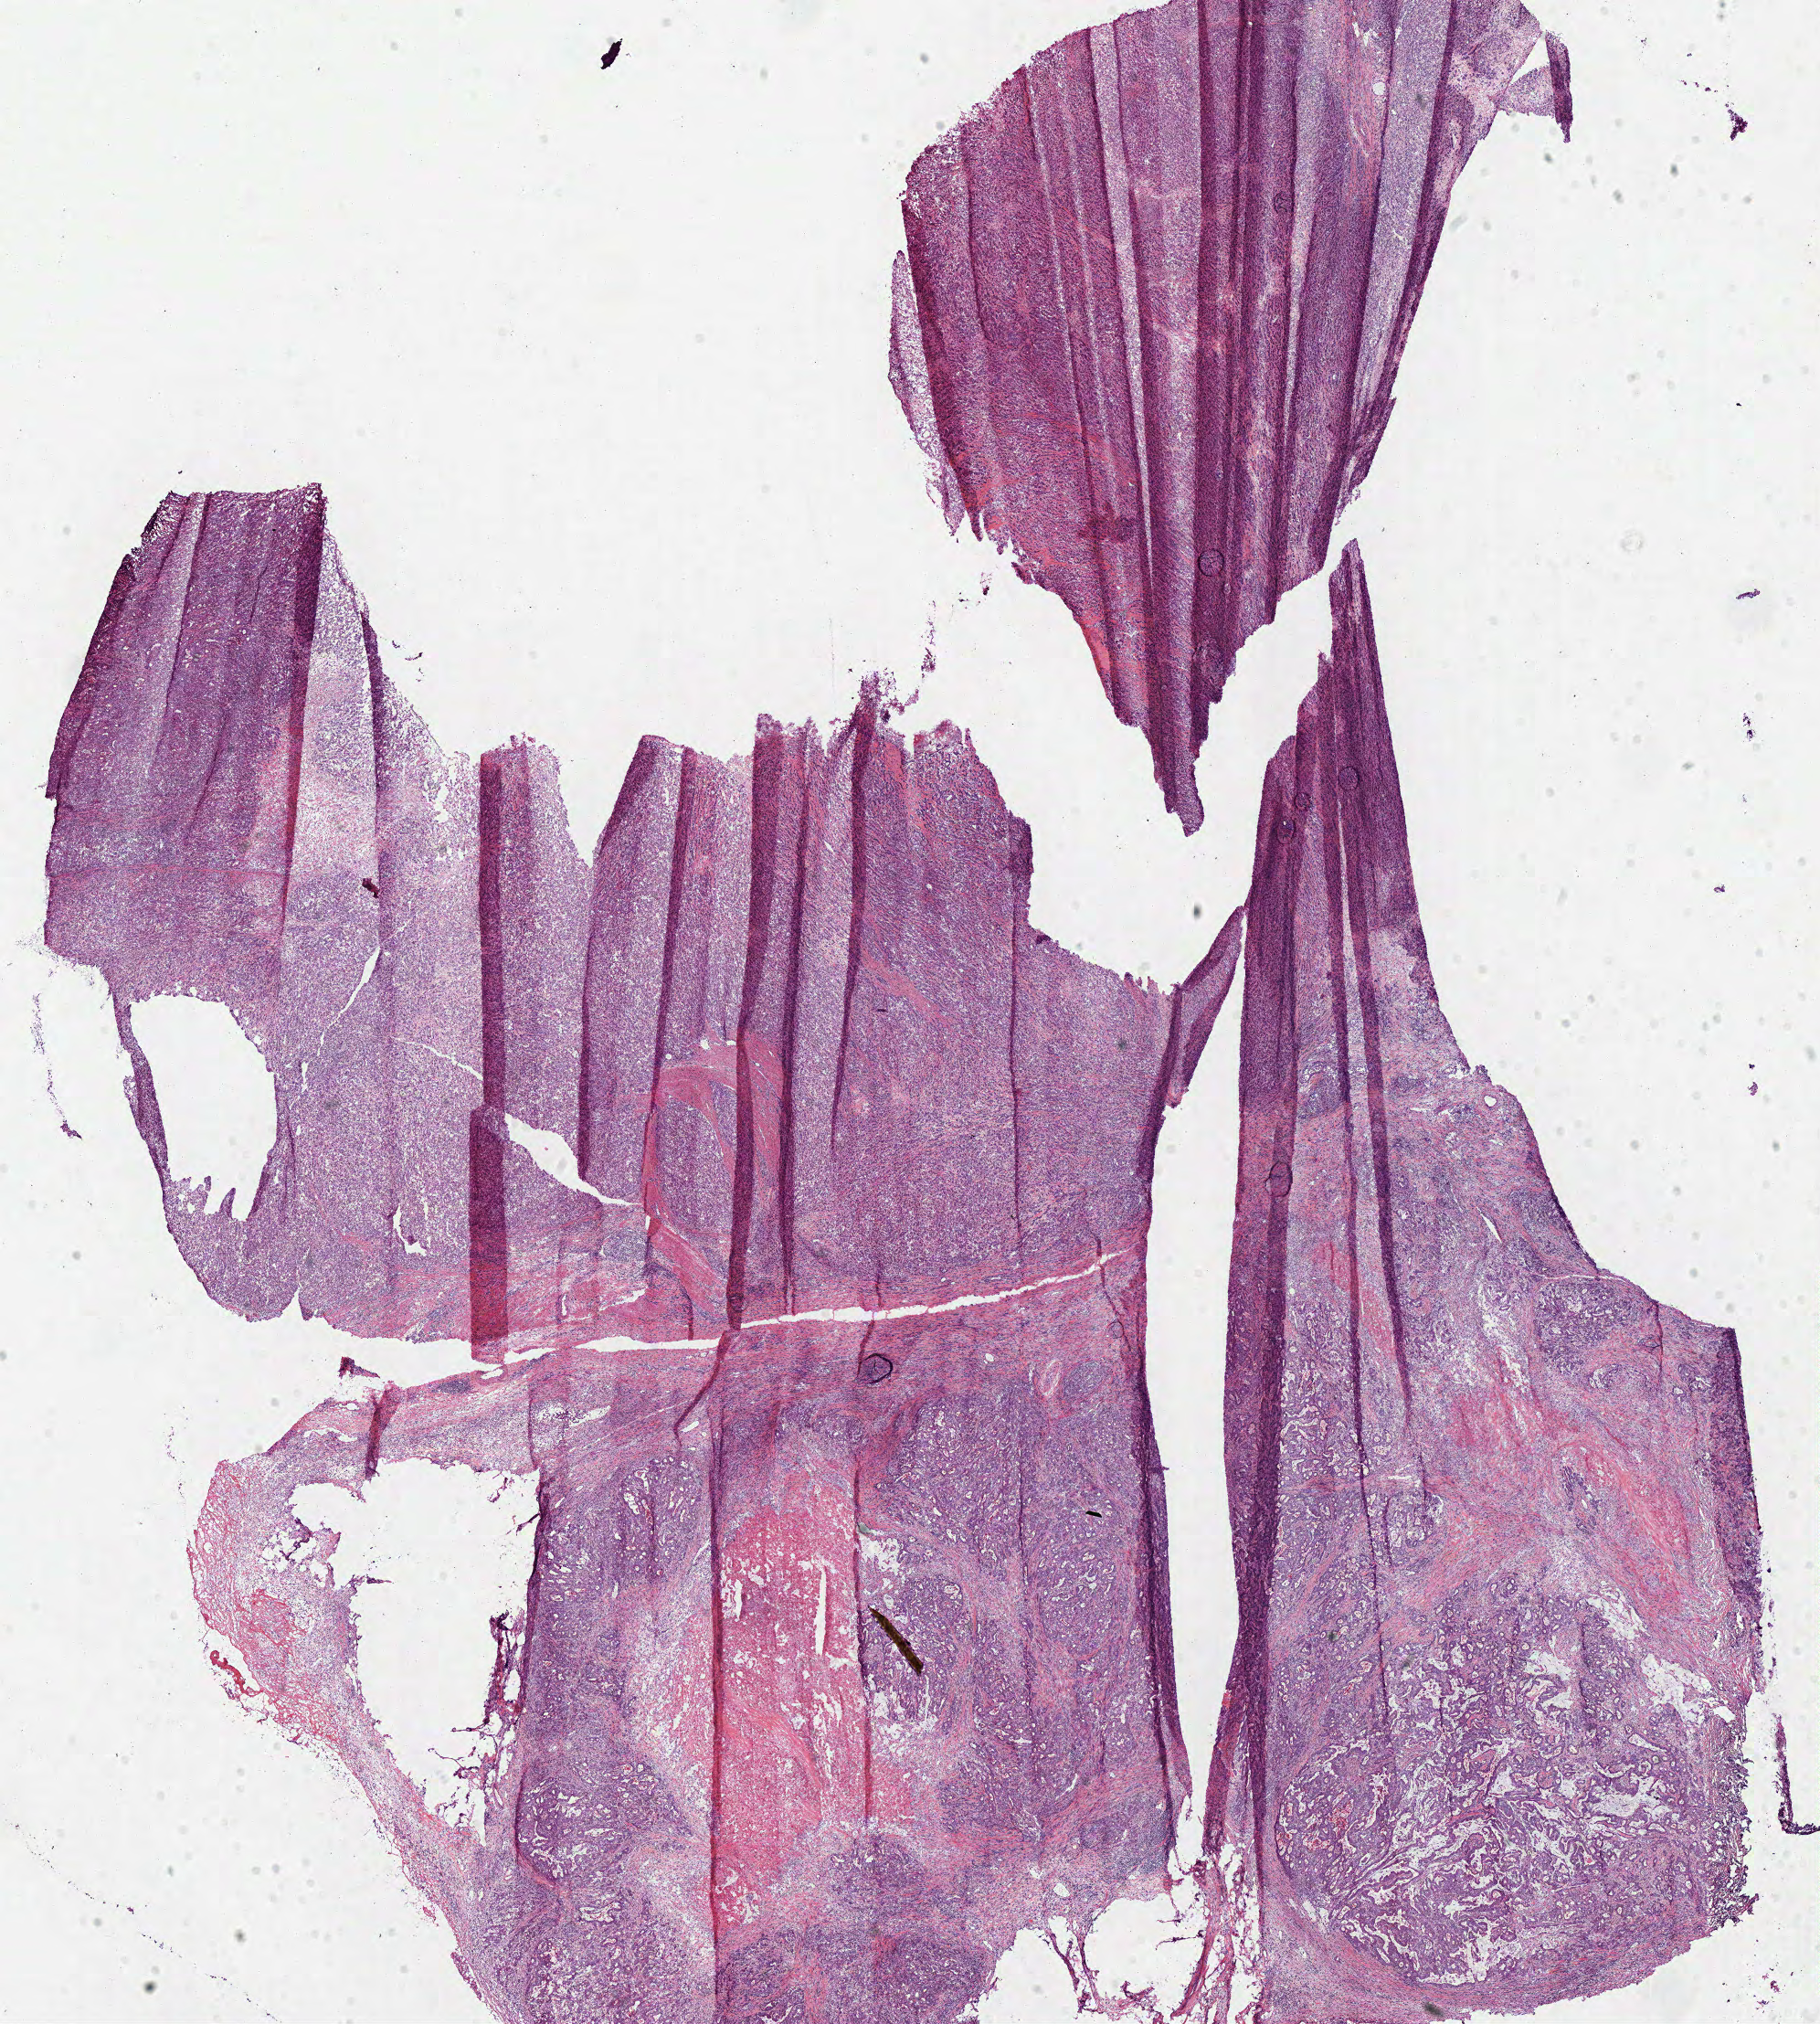
Whole-slide histology image, Hematoxylin and eosin (H&E) stained, whole scanned area (about 15.7 x 17.4 mm, from a 40x scan) shown as a low-resolution overview. Frozen section from the bottom of the tissue portion. Colon, primary tumour sample. Female, age 78 years at initial diagnosis. Composition of this section per pathologist review: tumour cells 80%, tumour nuclei 80%, normal cells 0%, stromal cells 10%, necrosis 10%.
Diagnosis: Adenocarcinoma, NOS. AJCC pathologic stage: IIA (7th edition). Lymph nodes positive (case pathology): 0 of 16 examined. TNM: T3 N0 M0.